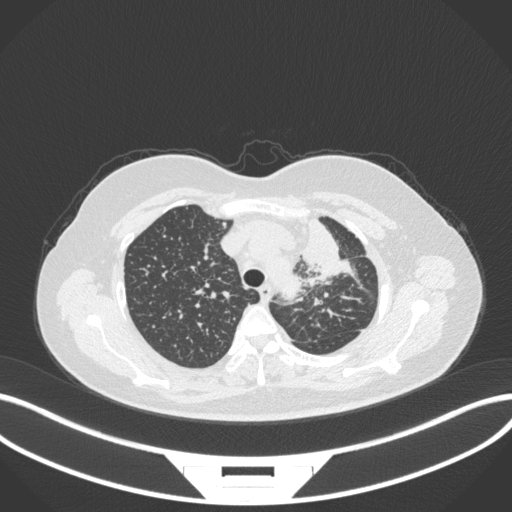
Chest CT, one axial slice; slice 260 of 348 in the series (ordered by position); reconstruction kernel B31f; 120 kVp; lung window (W 1500 / L -600 HU); 1 mm slice thickness; 512 × 512 image matrix, field of view 400 × 400 mm. Patient: female, 49 years. From the clinical record (not read from this slice): clinical TNM (as recorded): T1c N0 M1.
Annotated regions visible in this slice (bounding box drawn by a radiologist):
- lung tumour (recorded histology: adenocarcinoma): bounding box [x1, y1, x2, y2] px = [296, 213, 348, 286]